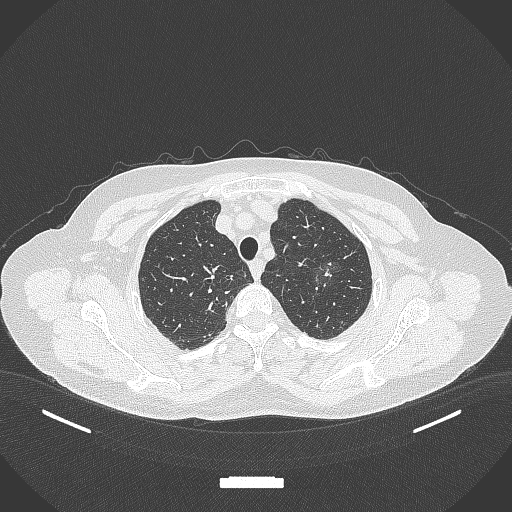
Chest CT, one axial slice; reconstruction kernel B70f; 120 kVp; lung window (W 1500 / L -600 HU); 512 × 512 image matrix, field of view 400 × 400 mm. Female patient, age 64 years. From the clinical record (not read from this slice): clinical TNM (as recorded): T1c N0 M0; histopathological grade: G1.
Outlined on this slice (bounding box drawn by a radiologist):
- lung tumour (recorded histology: adenocarcinoma): box from (x=305, y=253) to (x=345, y=300) px